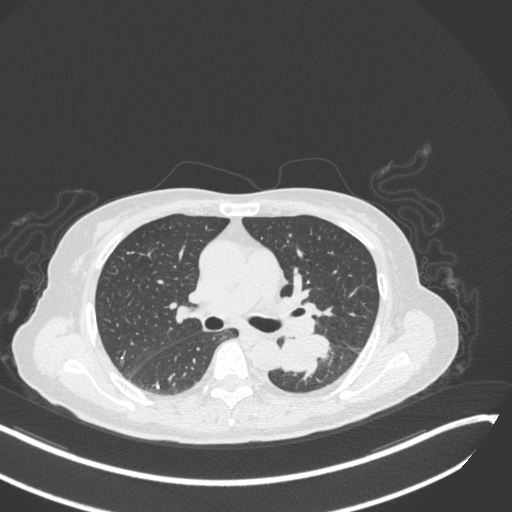
Chest CT, one axial slice; slice 168 of 342 in the series (ordered by position); lung window (W 1500 / L -600 HU); 1 mm slice thickness; 512 × 512 image matrix, field of view 400 × 400 mm. Patient: female, 64 years. Case-level facts recorded for this patient, not image findings: clinical TNM (as recorded): T3 N1 M1; histopathological grade: G3.
Annotated regions visible in this slice (rectangle marked by the reading radiologist):
- lung tumour (recorded histology: small cell carcinoma): bounding box (x1, y1, x2, y2) in pixels: (279, 333, 331, 379)